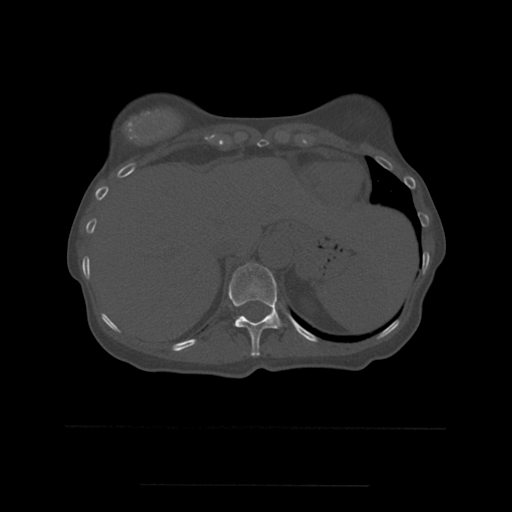
CT including the spine, one axial slice. Position 279 of 544 along the scan axis. Bone window (W 1800 / L 400 HU). 1.25 mm slice thickness. 512 × 512 image matrix, field of view 350 × 350 mm. Patient age 58 years. From the clinical record (not read from this slice): primary cancer: lung.
Structures marked on this image (semi-automatic segmentation, software-assisted and operator-edited):
- T11 vertebra: box from (x=229, y=263) to (x=283, y=357) px